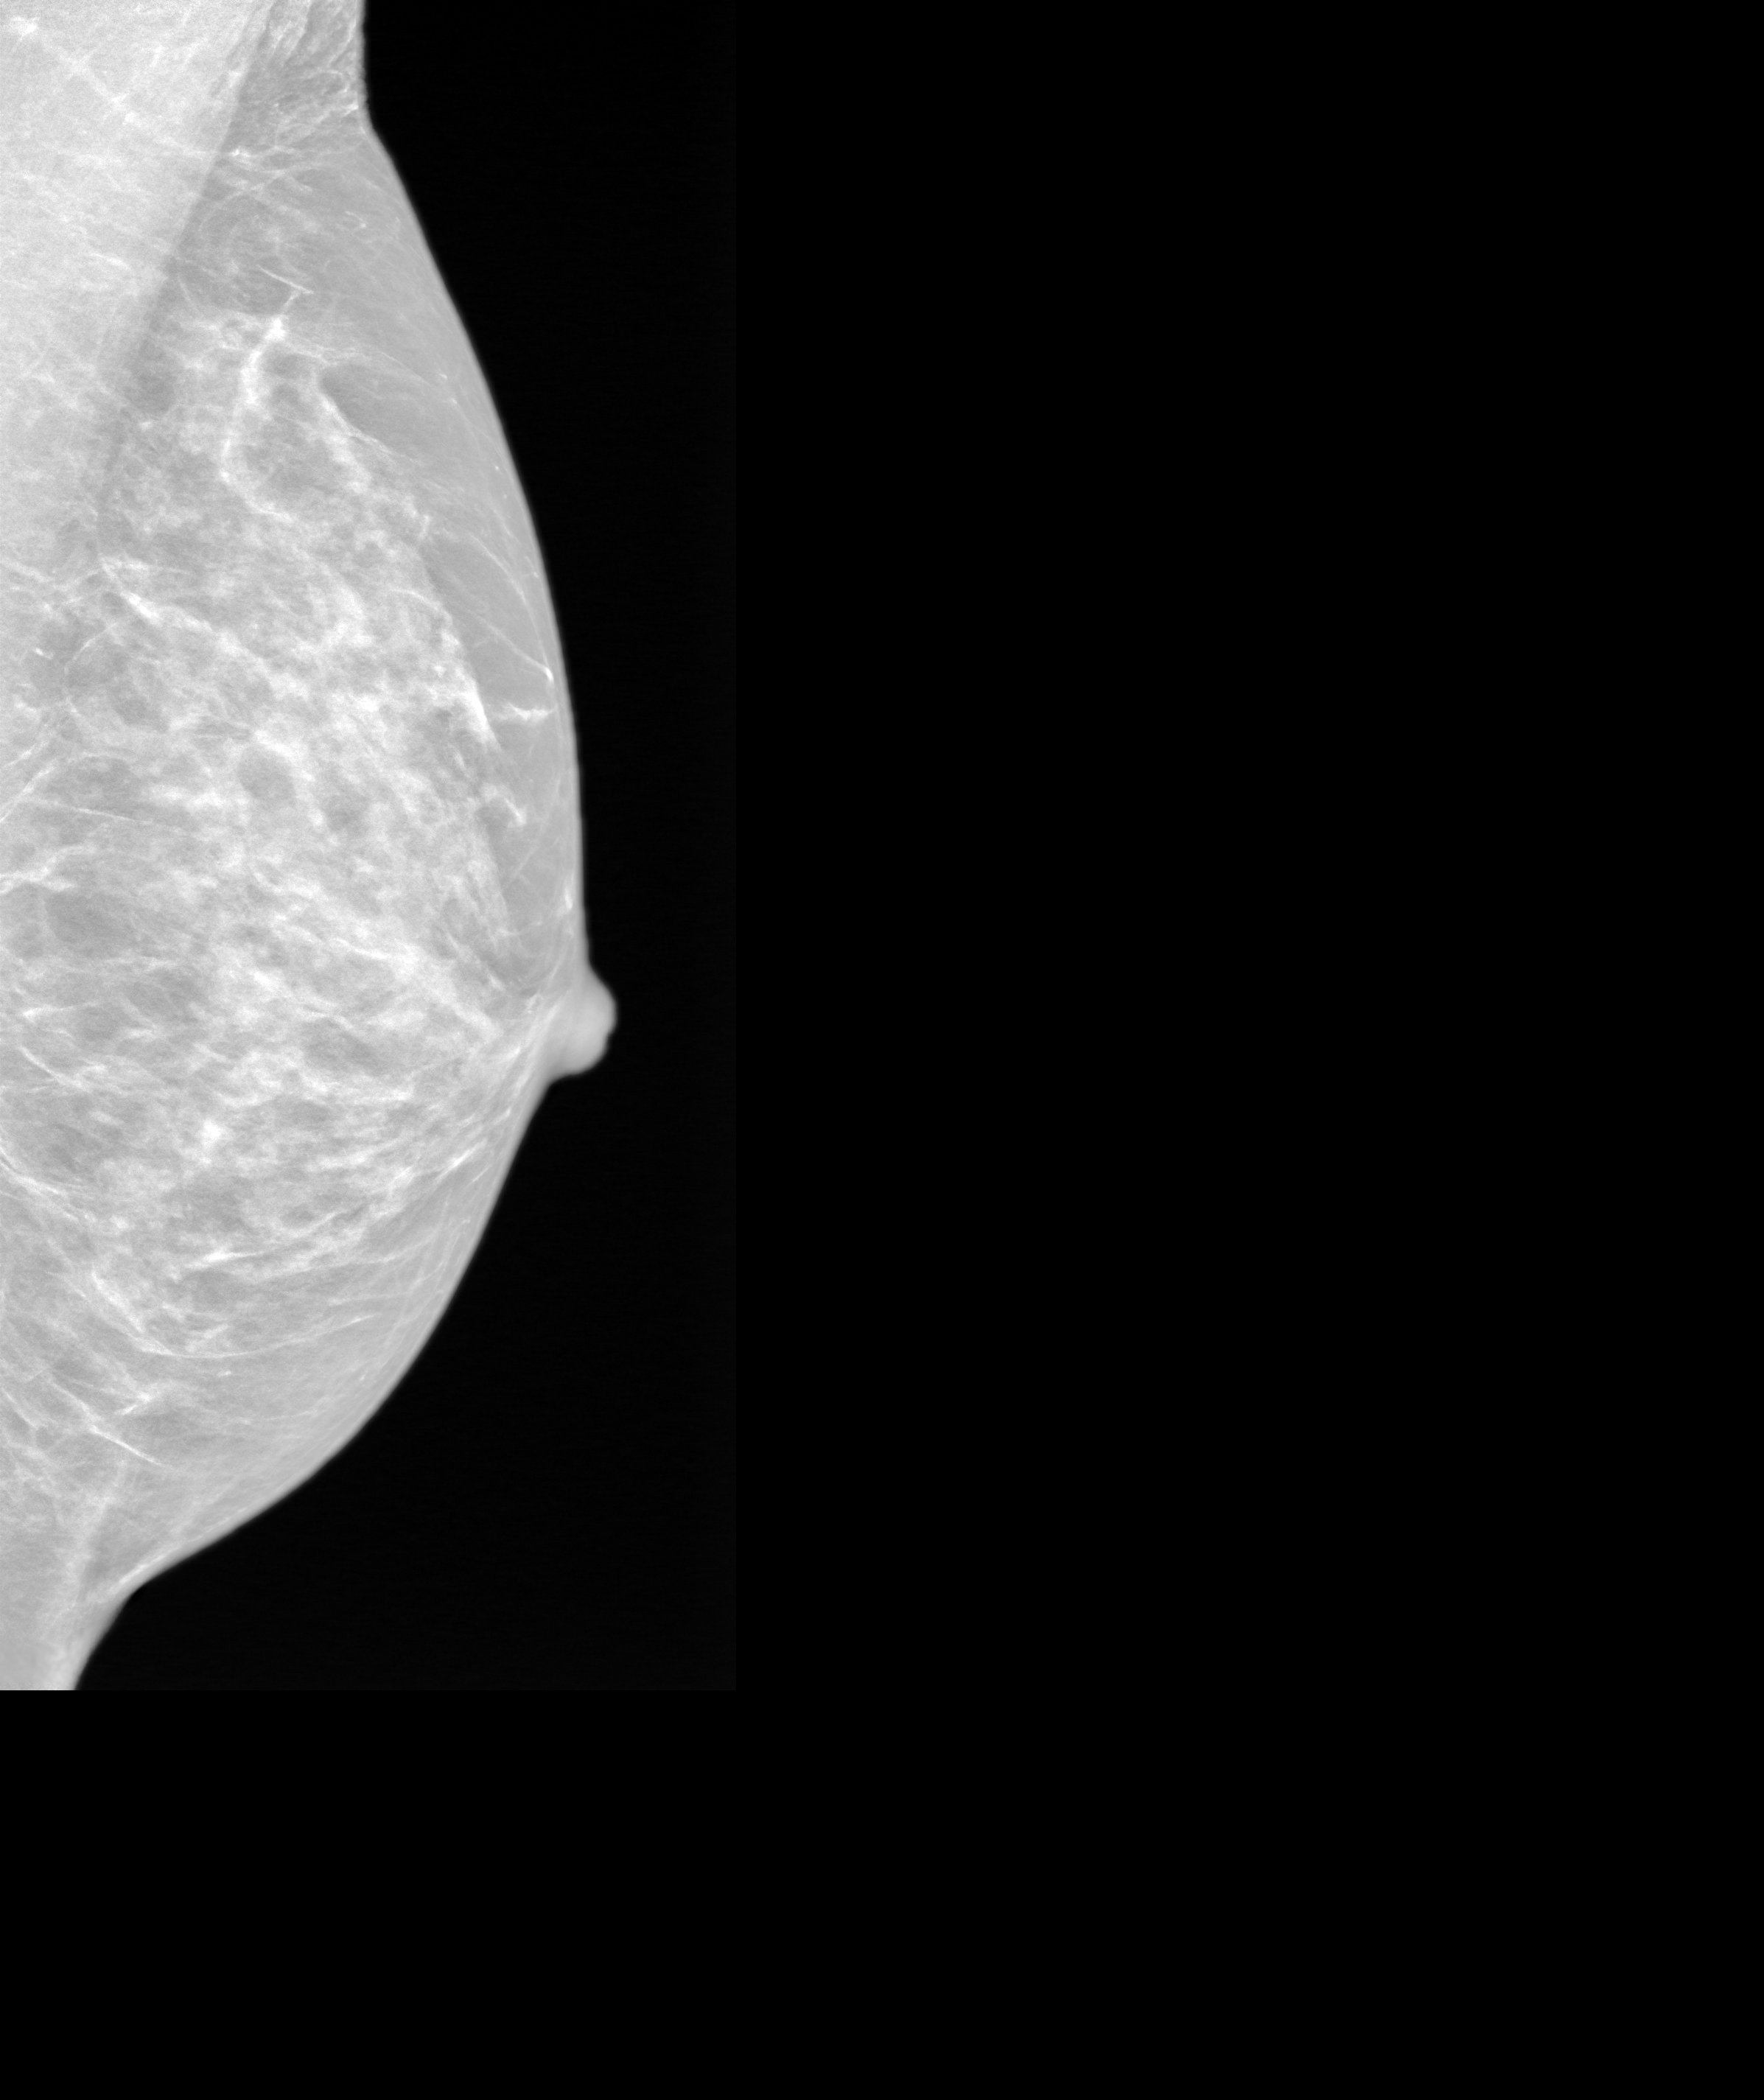
Annual screening mammography examination; system: SenoIris_1SP2(440). Female patient, age 57 years.
Image type: synthesized 2-D view from tomosynthesis. Breast: left. Projection: MLO view.